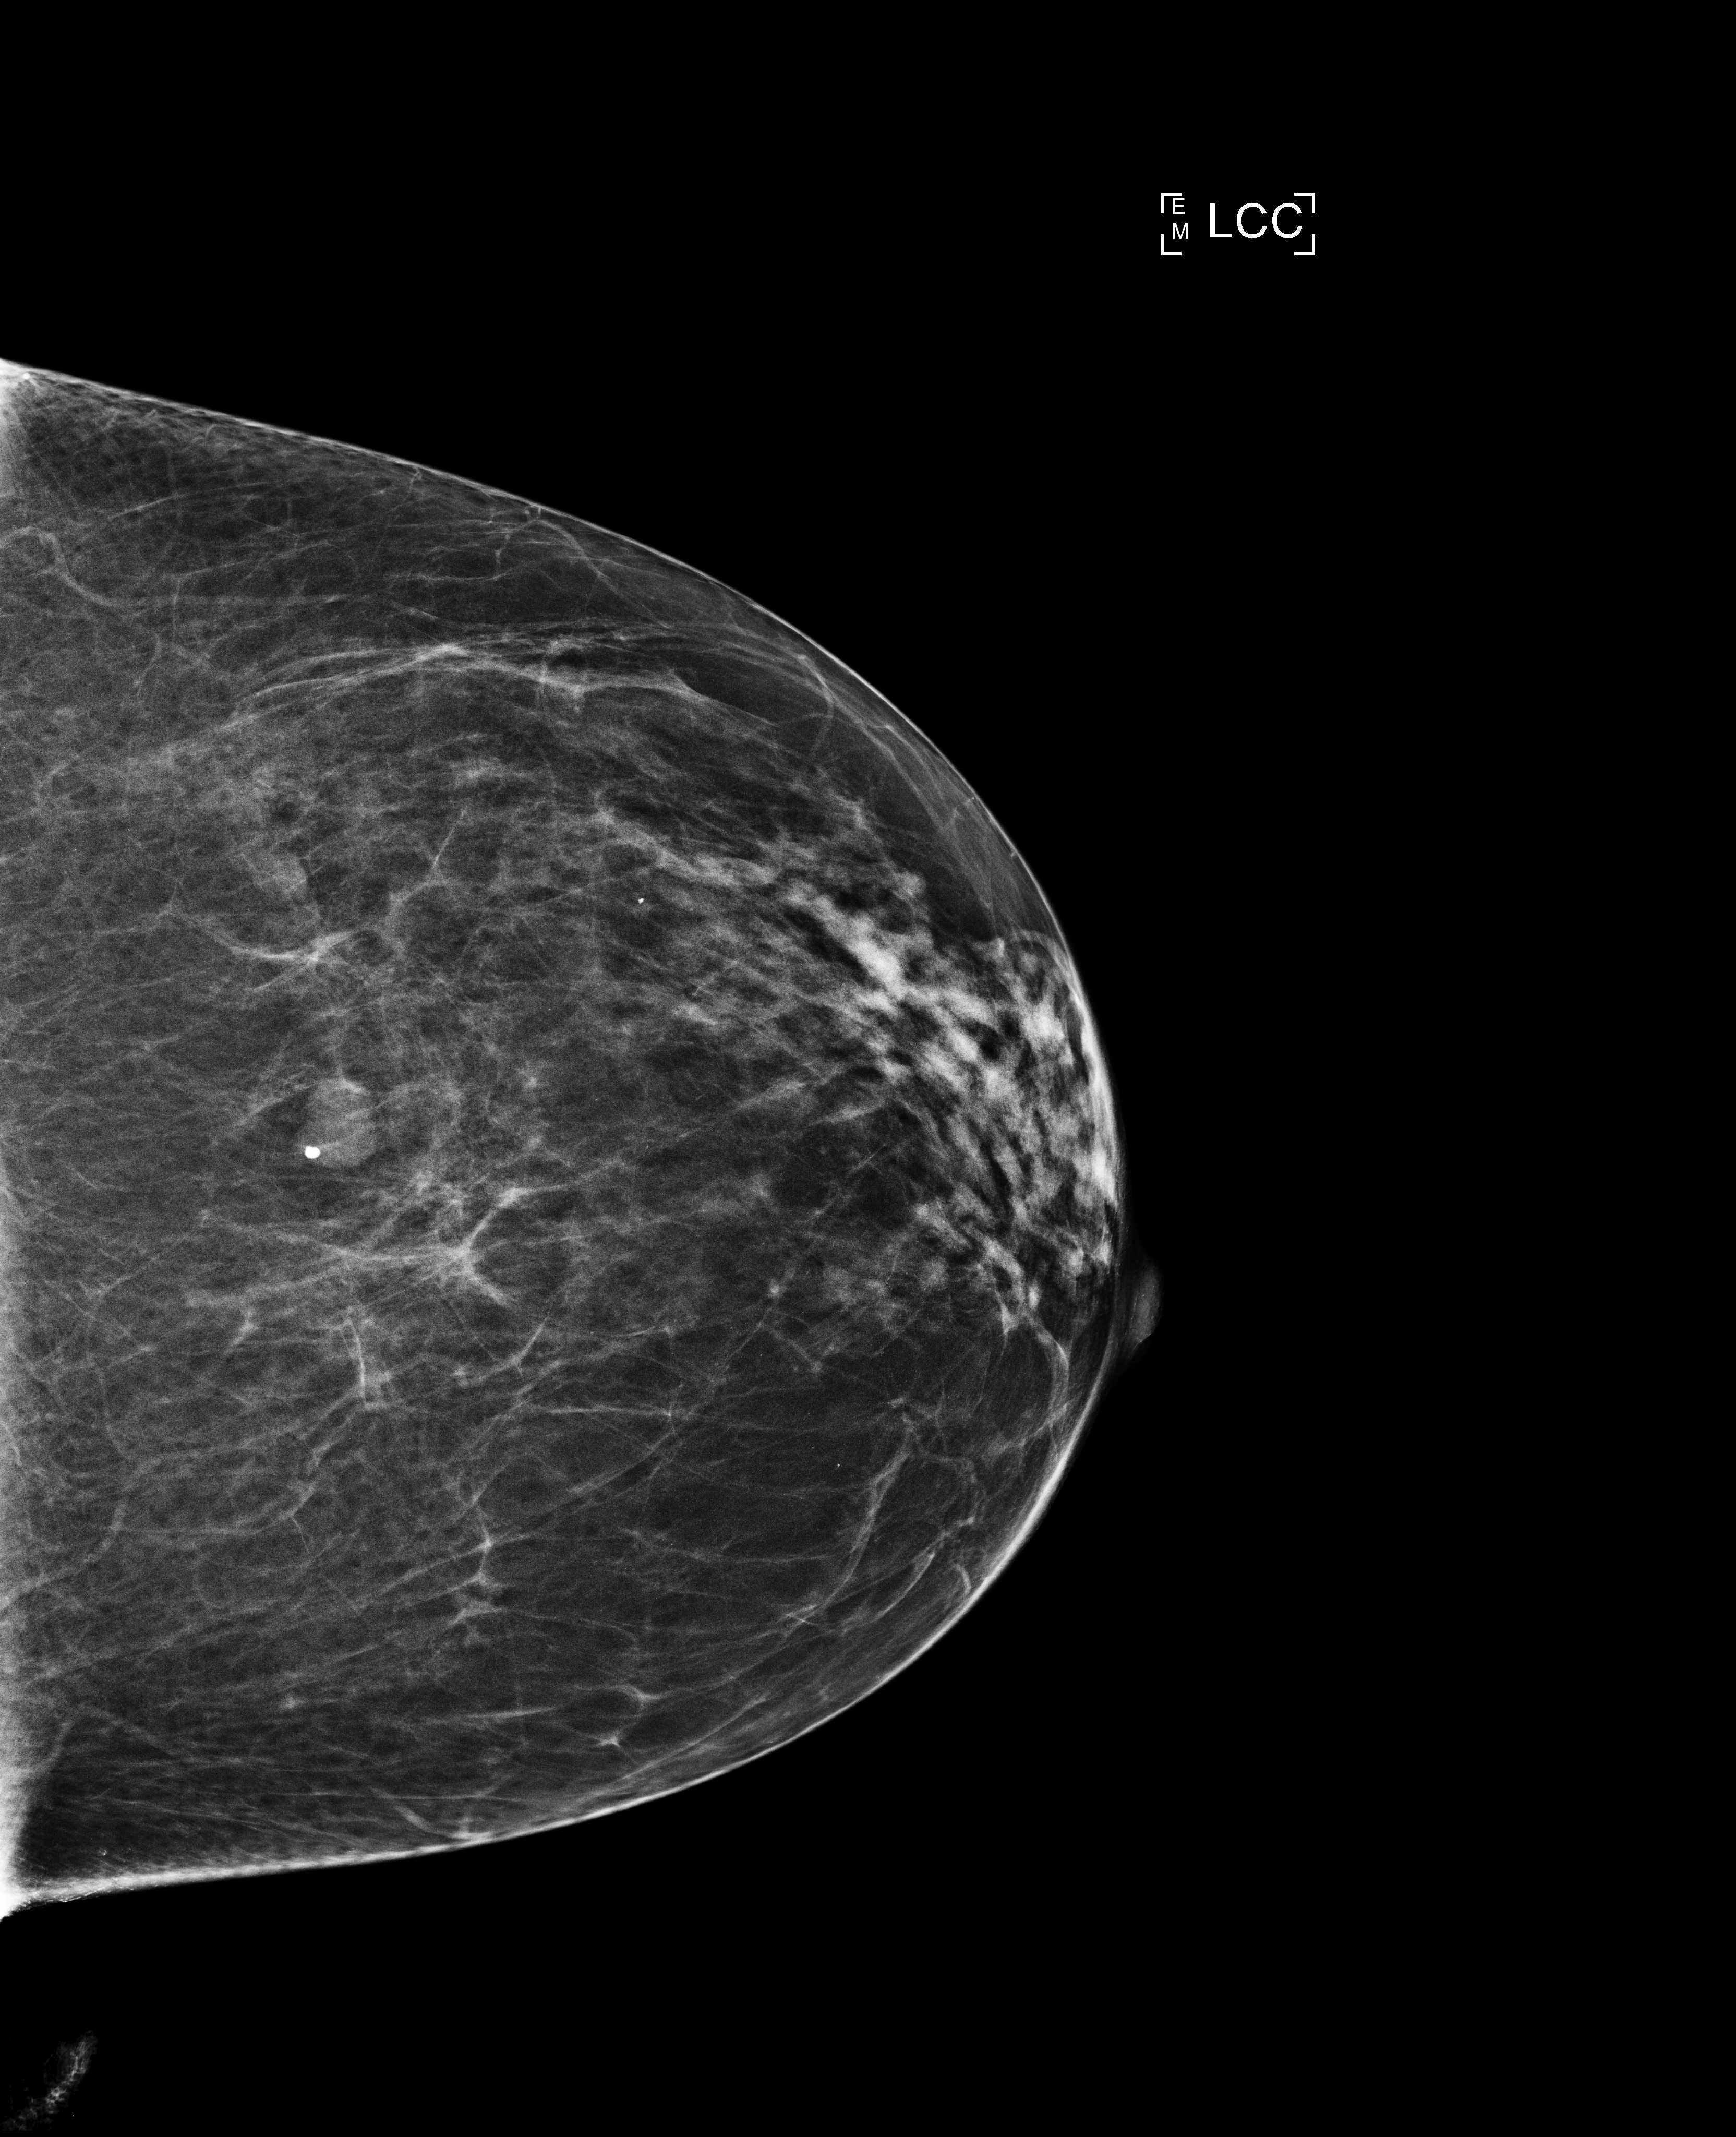
Full-field digital mammogram (FFDM), left breast, cranio-caudal projection, annual screening mammography examination, compressed breast thickness 58 mm, system: Selenia Dimensions. Patient aged 64 years (female).
- breast density at the screening exam (both breasts): scattered fibroglandular densities (BI-RADS density category b)
- final BI-RADS category for the screening round (tomosynthesis exam, both breasts): category 2
- recall: no recall after this screen